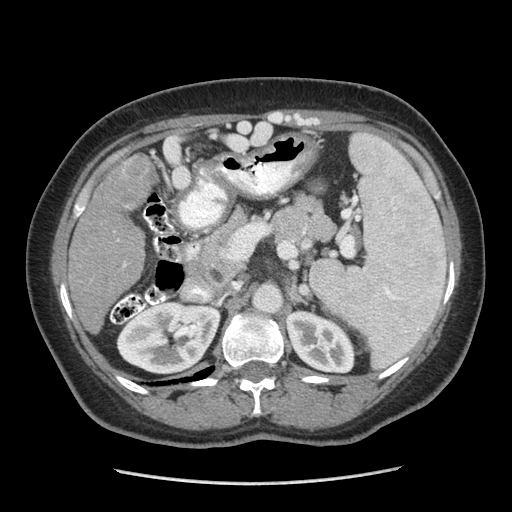
Contrast-enhanced abdominal CT (liver protocol), one axial slice; reconstruction kernel STANDARD; soft-tissue window (W 400 / L 40 HU); 2.5 mm slice thickness; 512 × 512 image matrix, field of view 360 × 360 mm. Case-level facts recorded for this patient, not image findings: diagnosis: hepatocellular carcinoma (patient treated with transarterial chemoembolisation; whether this scan precedes or follows treatment is not stated here); TNM stage (as recorded): Stage-I; Child-Pugh class: A; tumour differentiation: poorly differentiated.
Outlined on this slice (semi-automatically segmented with operator editing):
- liver parenchyma outside the tumour (the mass and vessels are separate outlines, so this box may not span the whole liver): bounding box <68,154,154,332> (left, top, right, bottom; pixels)
- mass: <93,156,158,215>